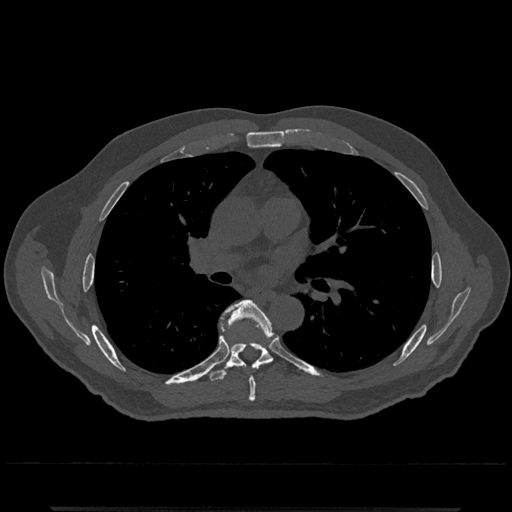
CT including the spine, one axial slice; position 746 of 797 along the scan axis; reconstruction kernel Br40s/3; bone window (W 1800 / L 400 HU); 512 × 512 image matrix, field of view 393 × 393 mm. Patient: male, 67 years. From the clinical record (not read from this slice): primary cancer: prostate.
Outlined on this slice (semi-automatically segmented with operator editing):
- T6 vertebra: bounding box (x1, y1, x2, y2) in pixels: (226, 300, 272, 402)
- T7 vertebra: (207, 310, 284, 383)